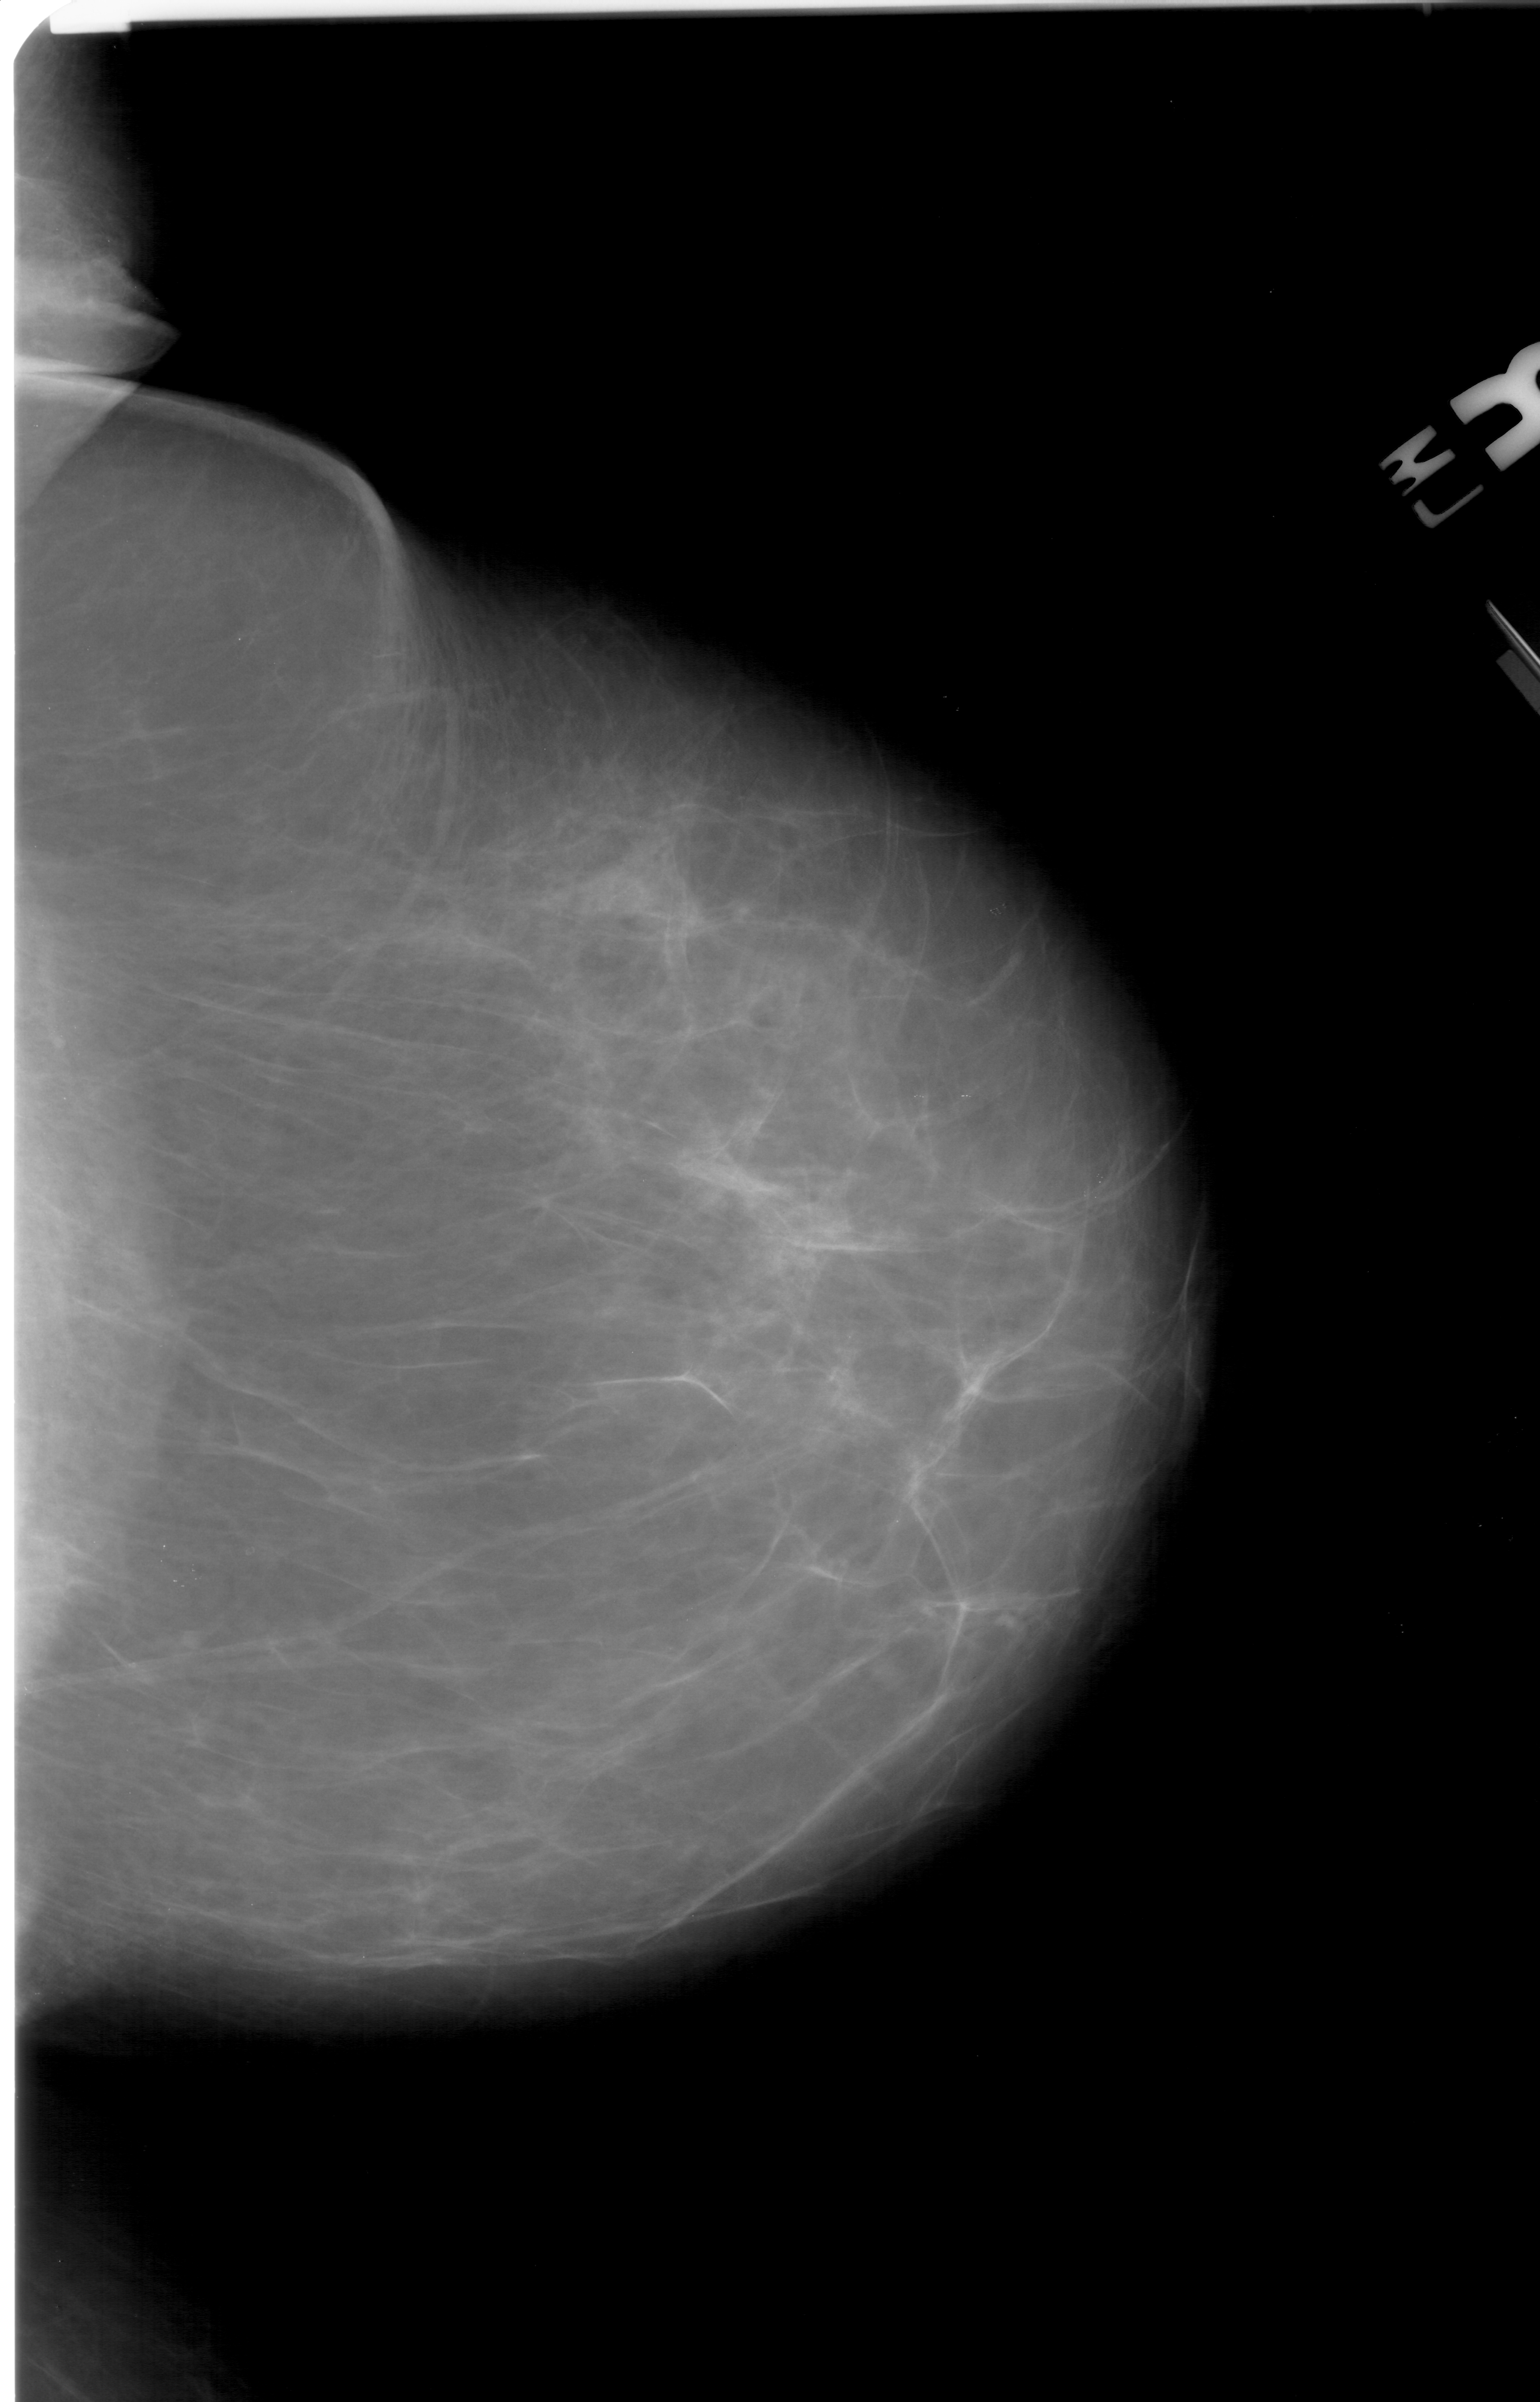
Scanned film-screen mammogram, right breast, CC view.
- Mass, shape oval, margins obscured; BI-RADS assessment category 4; subtlety rating 3 on a 1 (subtle) to 5 (obvious) scale; pathology (as recorded): benign.